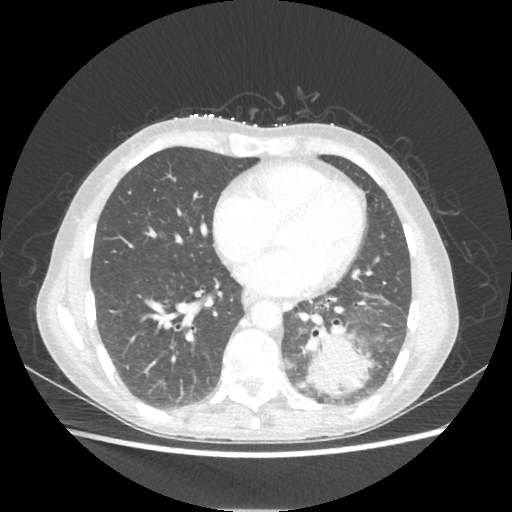
Chest CT, one axial slice. Slice 89 of 221 in the series (ordered by position). Reconstruction kernel STANDARD. Lung window (W 1500 / L -600 HU). 1.25 mm slice thickness. 512 × 512 image matrix, field of view 360 × 360 mm. Female patient, age 53 years. From the clinical record (not read from this slice): clinical TNM (as recorded): T3 N0 M0.
Structures marked on this image (bounding box drawn by a radiologist):
- lung tumour (recorded histology: adenocarcinoma): bounding box (x1, y1, x2, y2) in pixels: (305, 328, 372, 396)